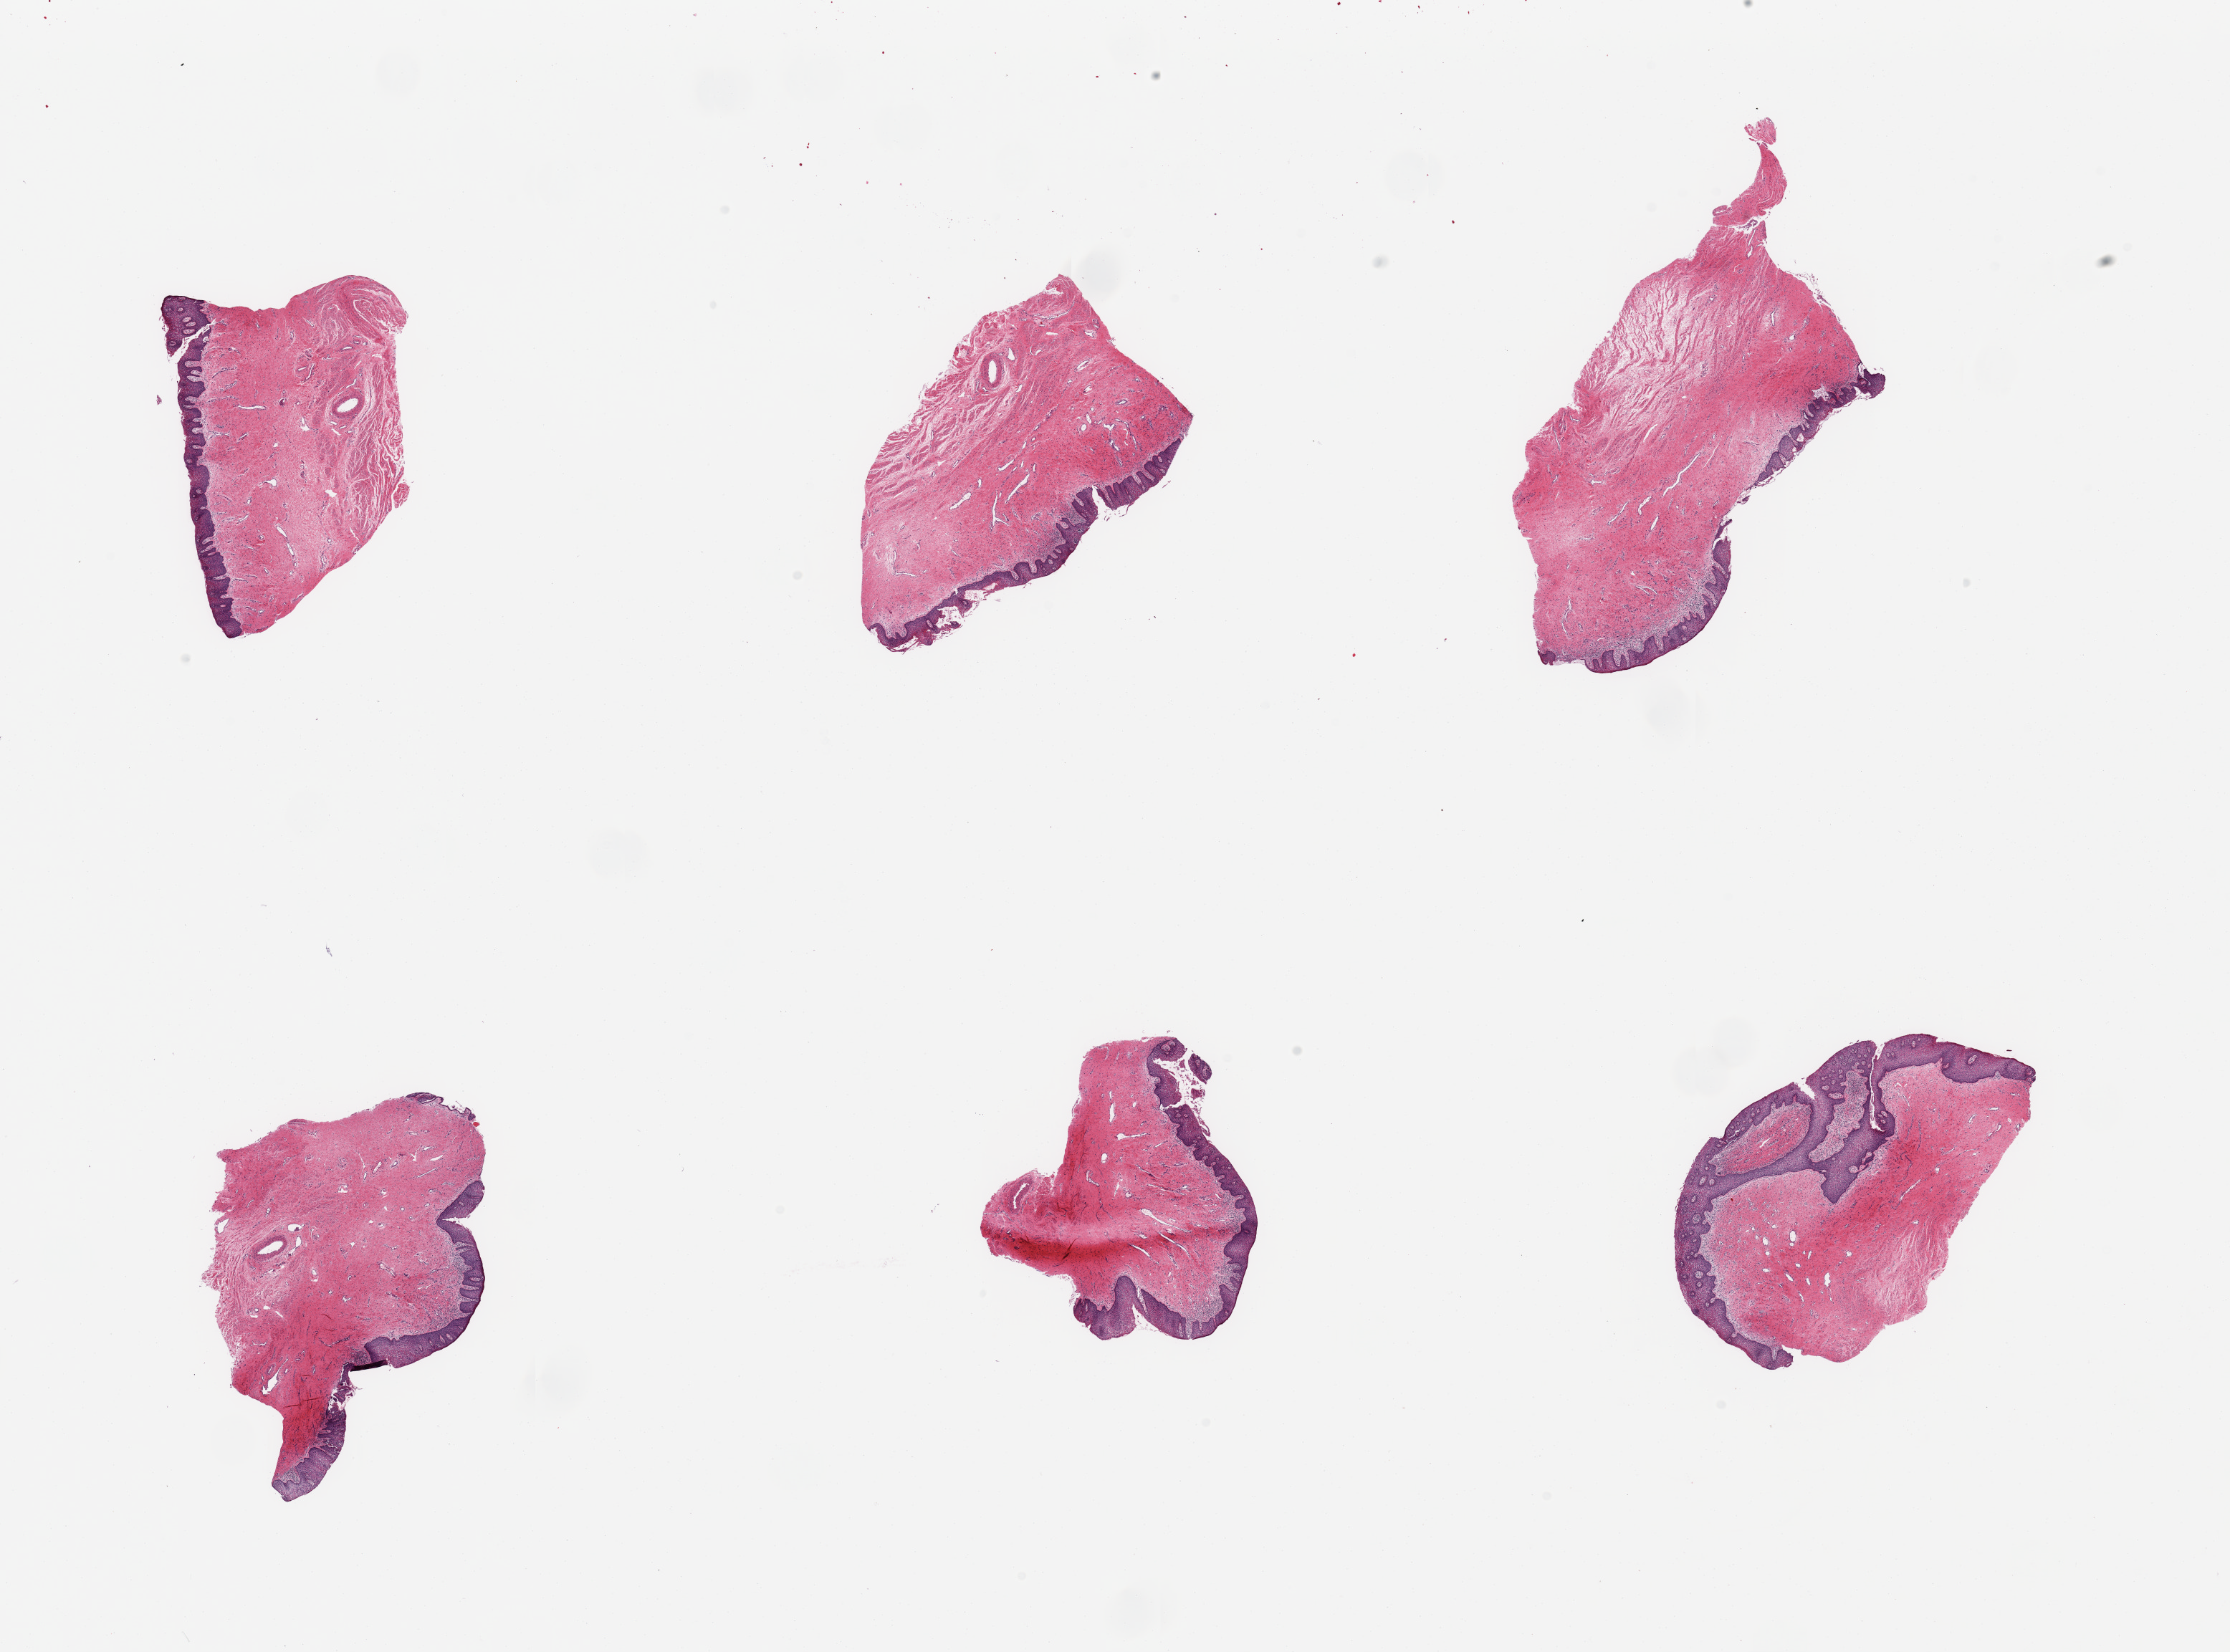
H&E whole-slide image, low-resolution overview of the scanned area, about 24.6 x 18.2 mm. PAXgene-fixed paraffin-embedded (PFPE) section. Section of vagina (target tissue). Tissue donor sample.
Reviewer comment on this tissue sample: 6 pieces; foci of chronic inflammation.